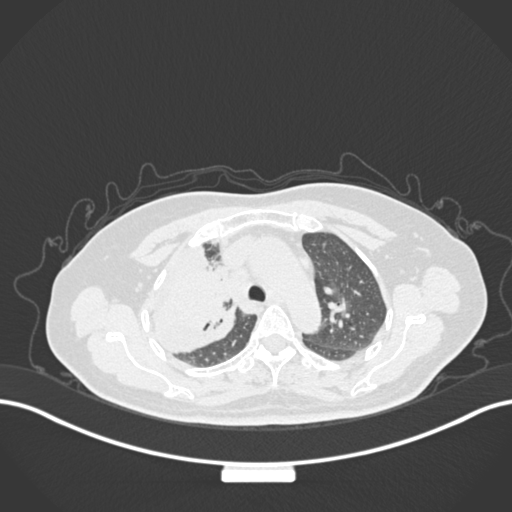
Chest CT, one axial slice. Slice 114 of 177 in the series (ordered by position). Reconstruction kernel B30f. Lung window (W 1500 / L -600 HU). 1 mm slice thickness. 512 × 512 image matrix, field of view 400 × 400 mm. Patient: female, 60 years. From the clinical record (not read from this slice): clinical TNM (as recorded): T3 N1 M1.
Structures marked on this image (rectangle marked by the reading radiologist):
- lung tumour (recorded histology: adenocarcinoma): bounding box (x1, y1, x2, y2) in pixels: (141, 236, 241, 356)